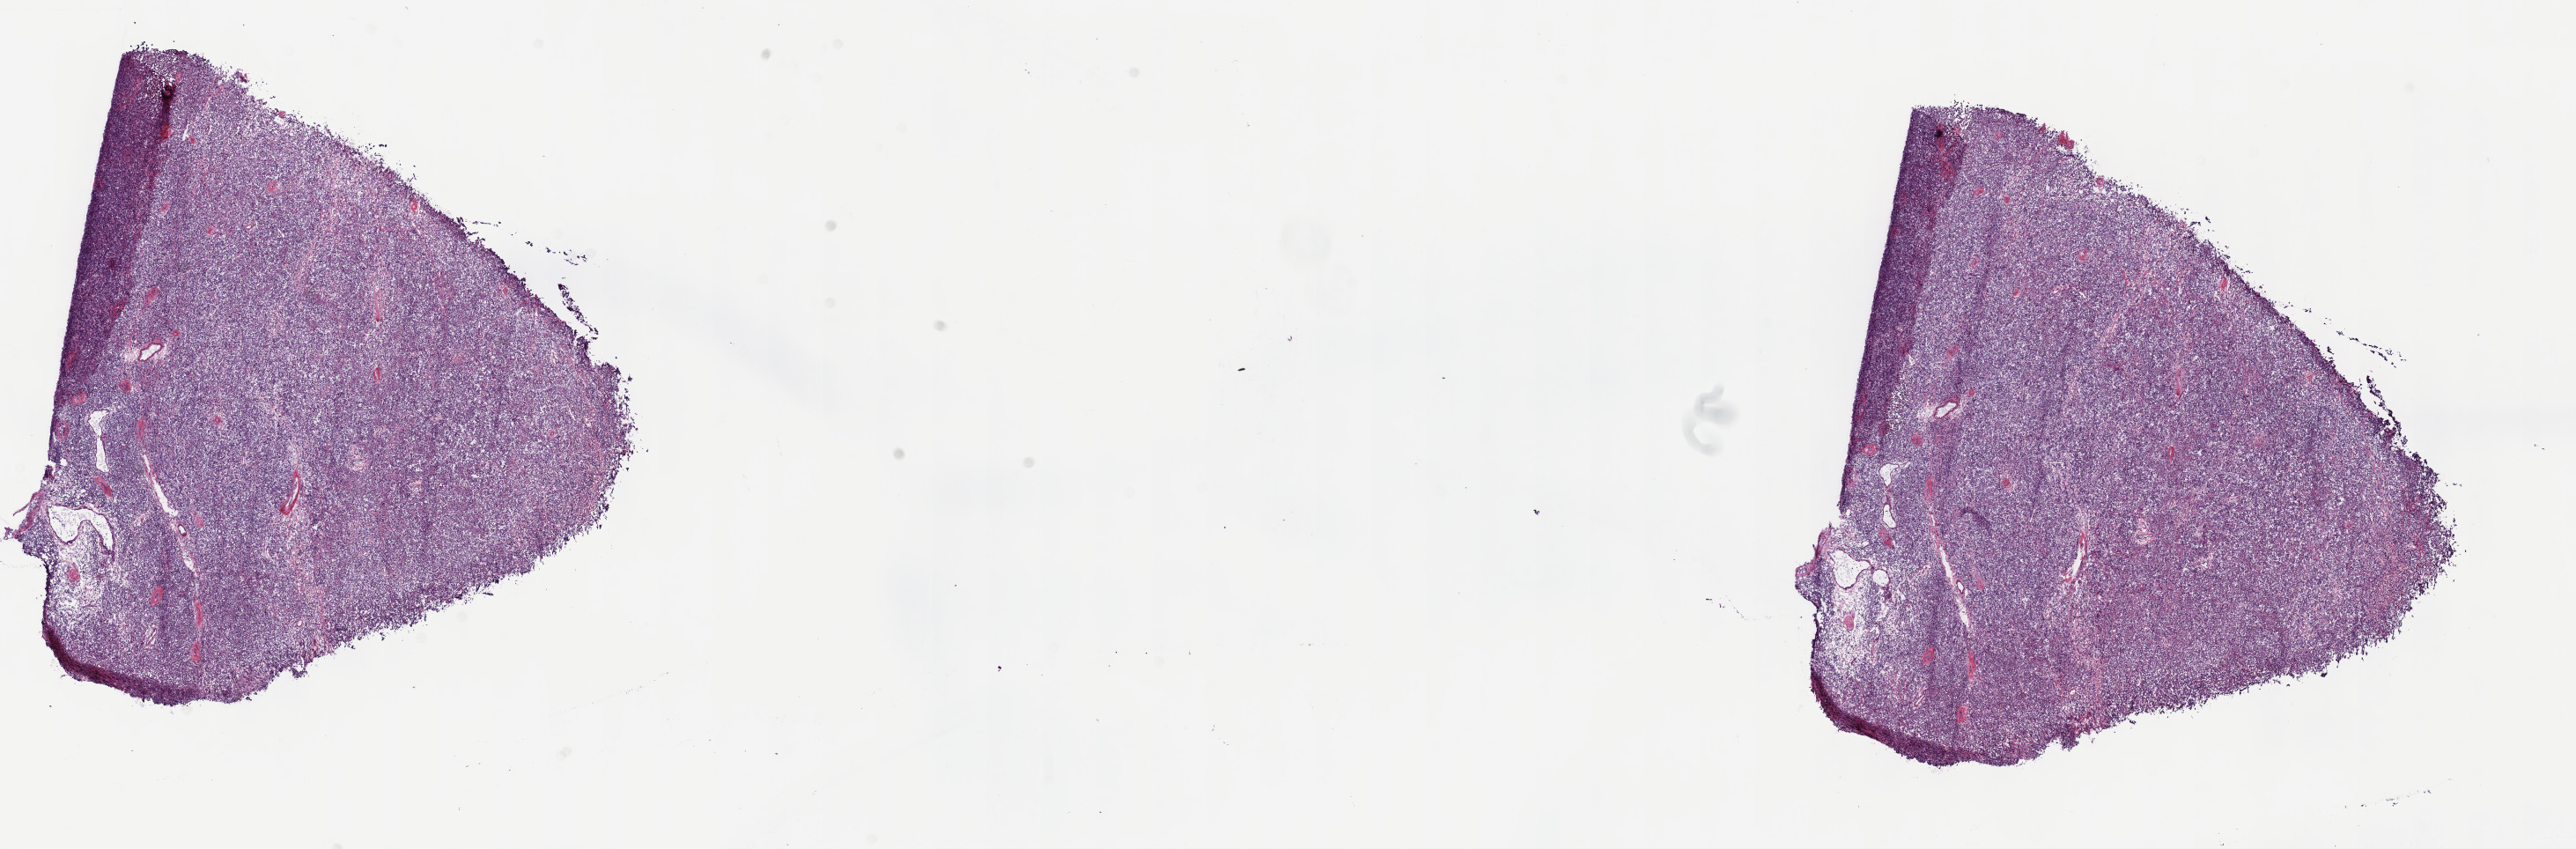
Hematoxylin and eosin (H&E) stained whole-slide image, a low-resolution overview of the entire scanned area, about 23.7 x 7.8 mm (acquisition: 40x scan), frozen section from the top of the tissue portion, primary tumour sample from the testis. Patient: male, age at initial diagnosis 31 years. Composition of this section per pathologist review: tumour cells 90%, tumour nuclei 70%, normal cells 0%, stromal cells 10%, necrosis 0%. Infiltration values recorded for this section: lymphocyte infiltration 90%, monocyte infiltration 10%, neutrophil infiltration 0%.
- AJCC pathologic stage: IS
- diagnosis: Seminoma, NOS
- TNM: T1 N0 M0